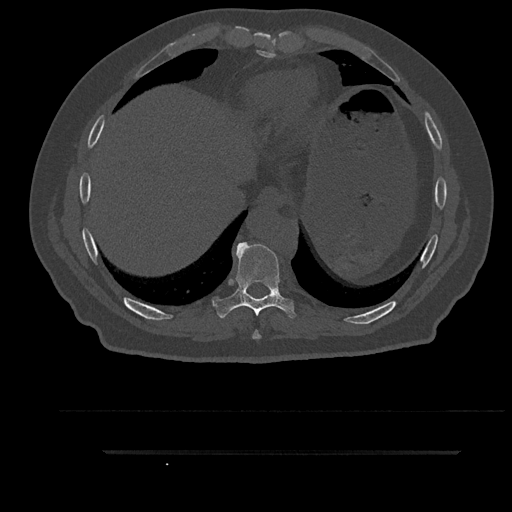
CT including the spine, one axial slice; slice 427 of 797 in the series (ordered by position); reconstruction kernel Br40s/3; bone window (W 1800 / L 400 HU); 0.5 mm slice thickness; 512 × 512 image matrix, field of view 432 × 432 mm. Male patient, age 63 years. Case-level facts recorded for this patient, not image findings: primary cancer: renal; vertebrae with lytic lesions (as recorded): T8.
Outlined on this slice (semi-automatic segmentation, software-assisted and operator-edited):
- T8 vertebra: bounding box (x1, y1, x2, y2) in pixels: (252, 330, 261, 339)
- T9 vertebra: (212, 242, 296, 318)